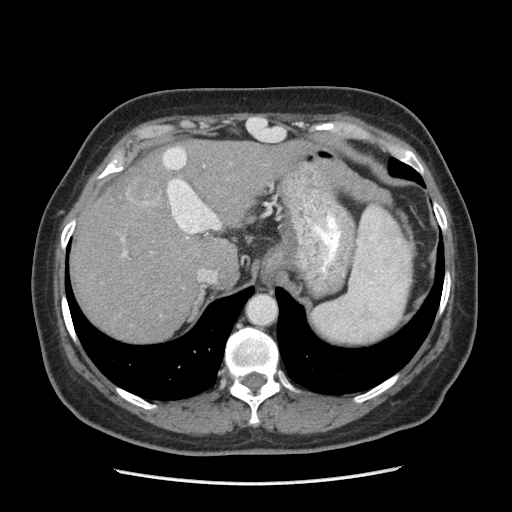
Contrast-enhanced abdominal CT (liver protocol), one axial slice. Slice 162 of 185 in the series (ordered by position). Soft-tissue window (W 400 / L 40 HU). 2.5 mm slice thickness. 512 × 512 image matrix, field of view 360 × 360 mm. From the clinical record (not read from this slice): diagnosis: hepatocellular carcinoma (patient treated with transarterial chemoembolisation; whether this scan precedes or follows treatment is not stated here); TNM stage (as recorded): Stage-I; Child-Pugh class: A; tumour differentiation: poorly differentiated.
Structures marked on this image (semi-automatically segmented with operator editing):
- abdominal aorta: box from (x=248, y=296) to (x=275, y=323) px
- liver parenchyma outside the tumour (the mass and vessels are separate outlines, so this box may not span the whole liver): (x=70, y=140)–(x=284, y=342)
- mass: (x=125, y=172)–(x=165, y=213)
- liver vessels: (x=123, y=208)–(x=220, y=256)